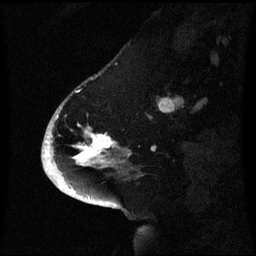
Breast MRI (dynamic contrast-enhanced), one sagittal slice; slice 19 of 60 in the series (ordered by position); dynamic contrast-enhanced series, image 2 of 3 at this slice position (ordered by acquisition); 1.5 T; TE 4.2 ms, TR 8.4 ms; 256 × 256 image matrix, field of view 220 × 220 mm. Patient: female, 53 years. Case-level facts recorded for this patient, not image findings: setting: breast cancer imaged before/during neoadjuvant chemotherapy; receptor status: HR-positive, HER2-negative.
Outlined on this slice (semi-automatic segmentation, software-assisted and operator-edited):
- analysis volume of interest (the breast-tissue region the enhancement analysis was run in; not a lesion): box from (x=52, y=102) to (x=131, y=171) px
- tumour enhancement mask (voxels above the 70 % enhancement threshold inside the analysis volume of interest): (x=52, y=134)–(x=116, y=169)